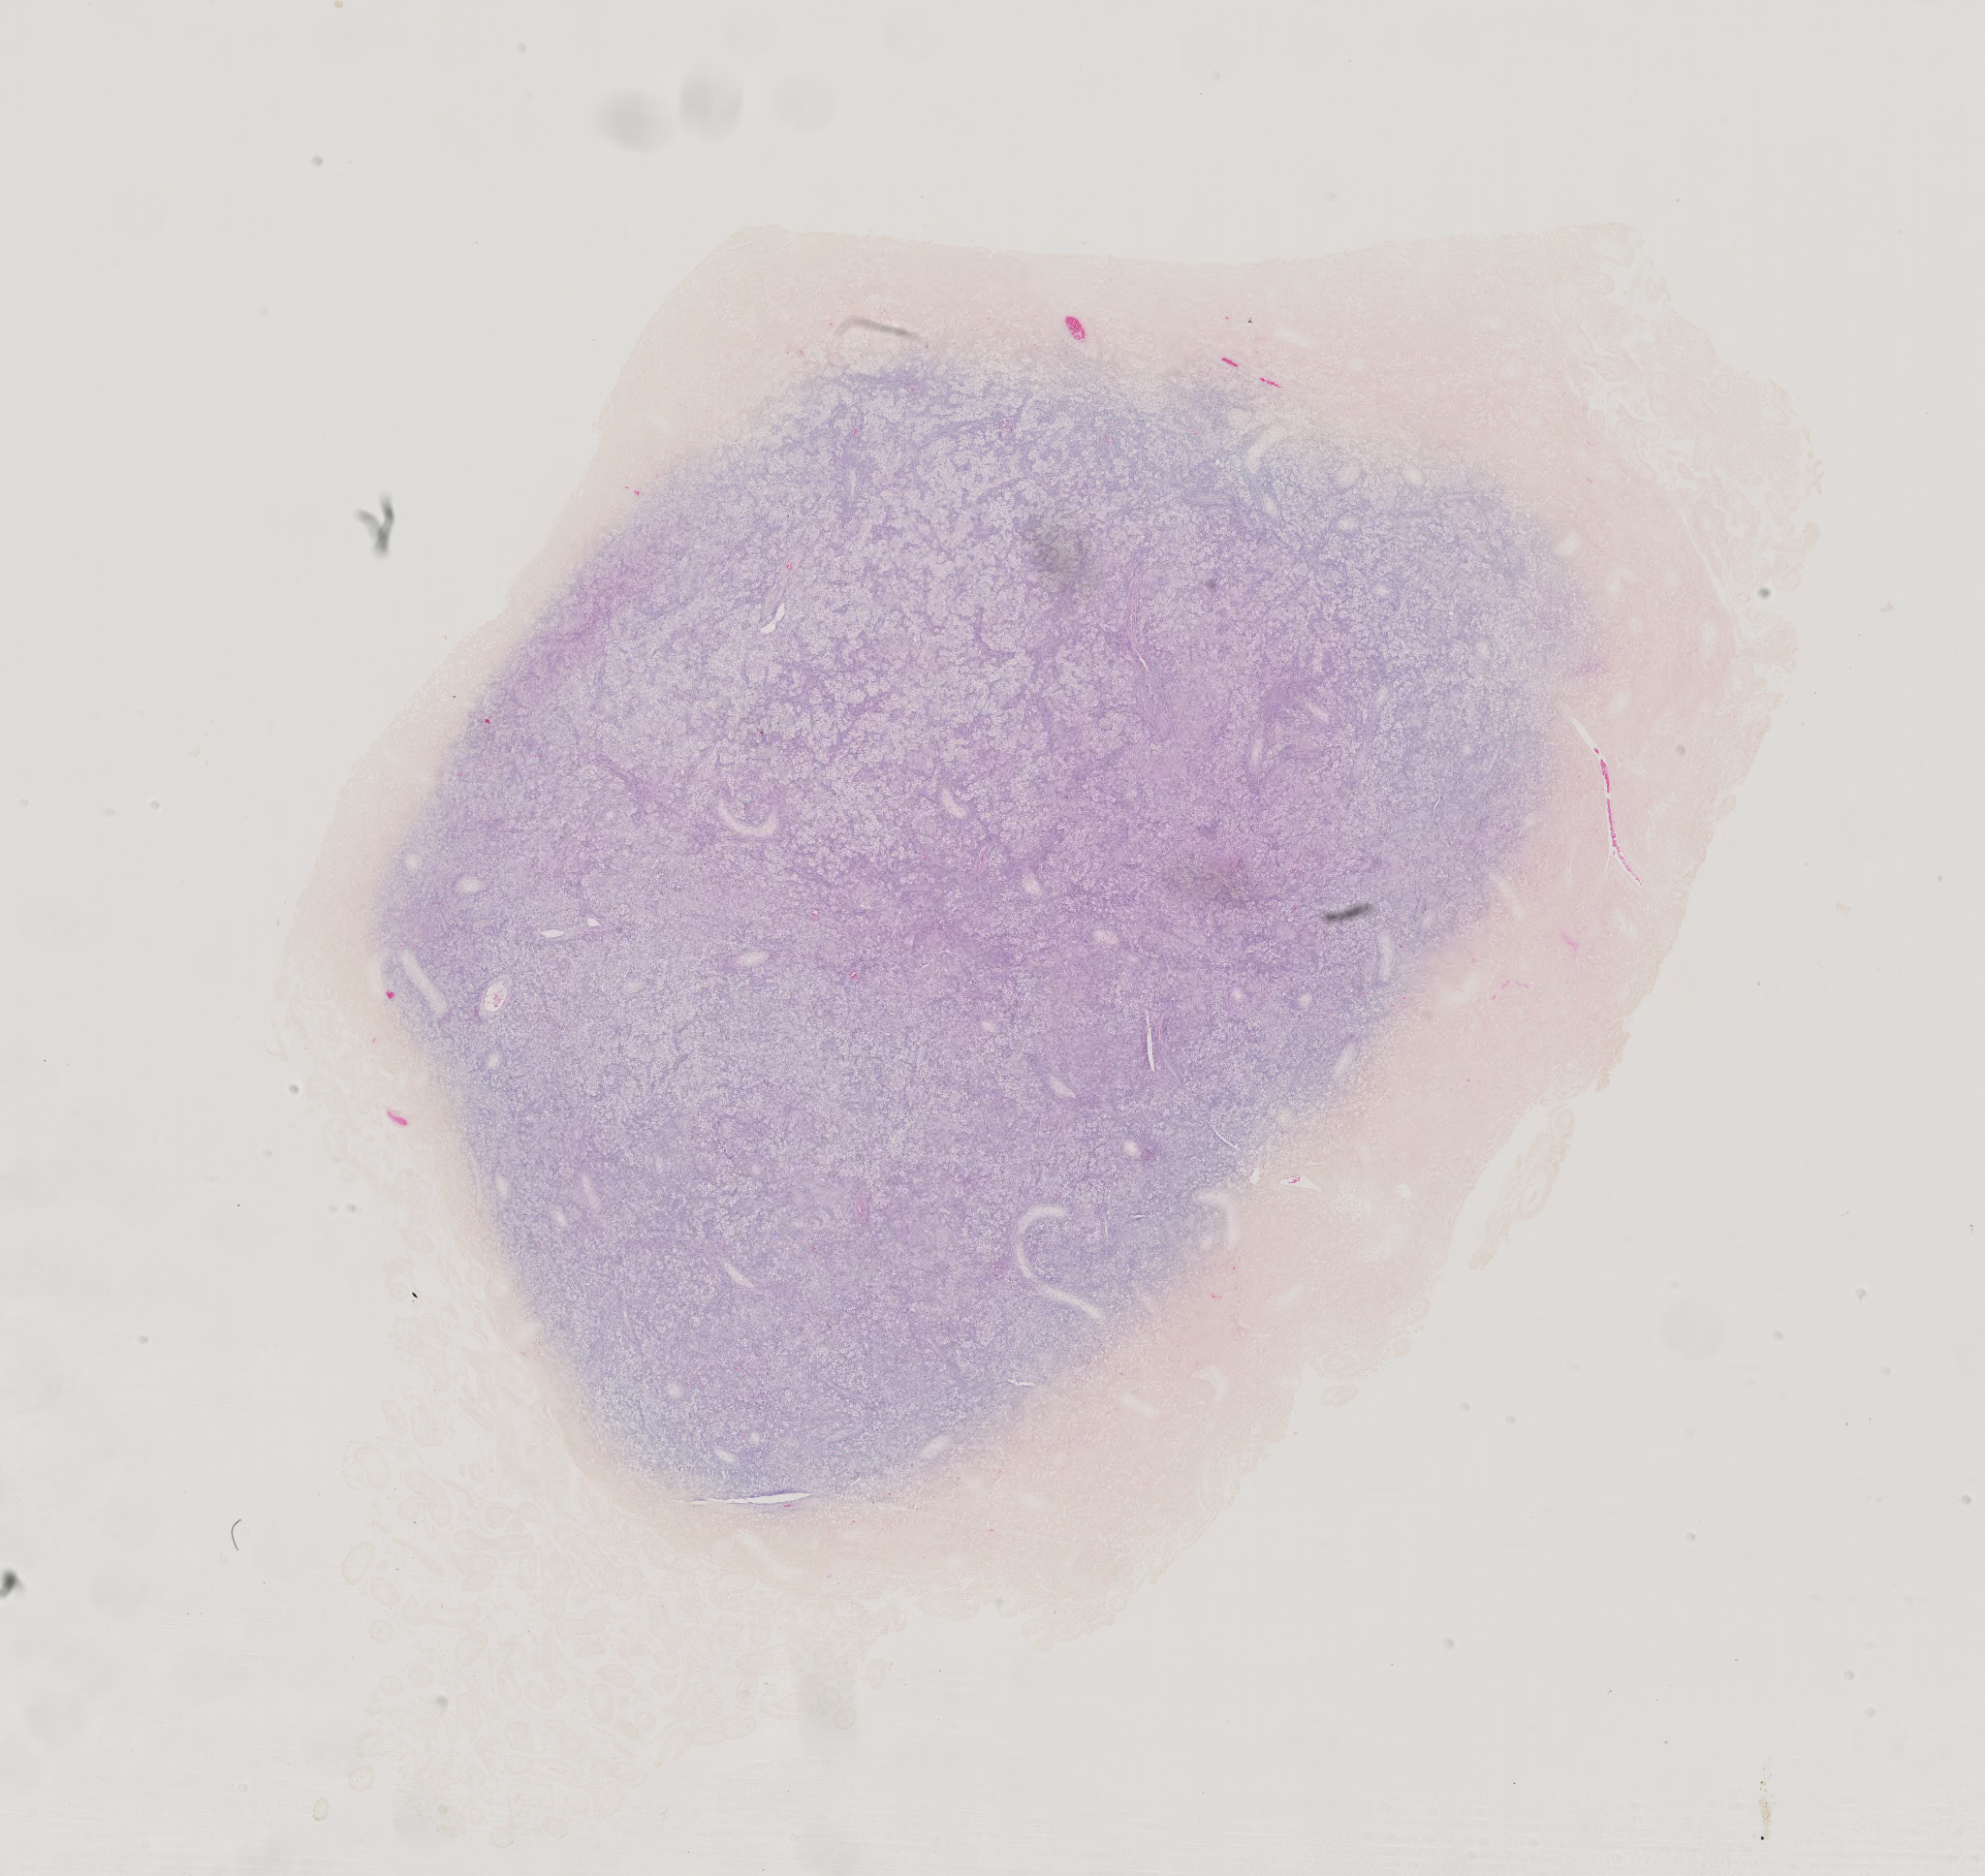
Hematoxylin and eosin (H&E) stained whole-slide image, shown as a low-resolution overview of the whole scanned area (about 14.9 x 14.1 mm, from a 40x scan); FFPE section; primary tumour sample from the testis. Male patient; age at initial diagnosis 32 years.
* AJCC pathologic stage: I (4th edition)
* laterality: left
* histologic diagnosis: Seminoma, NOS